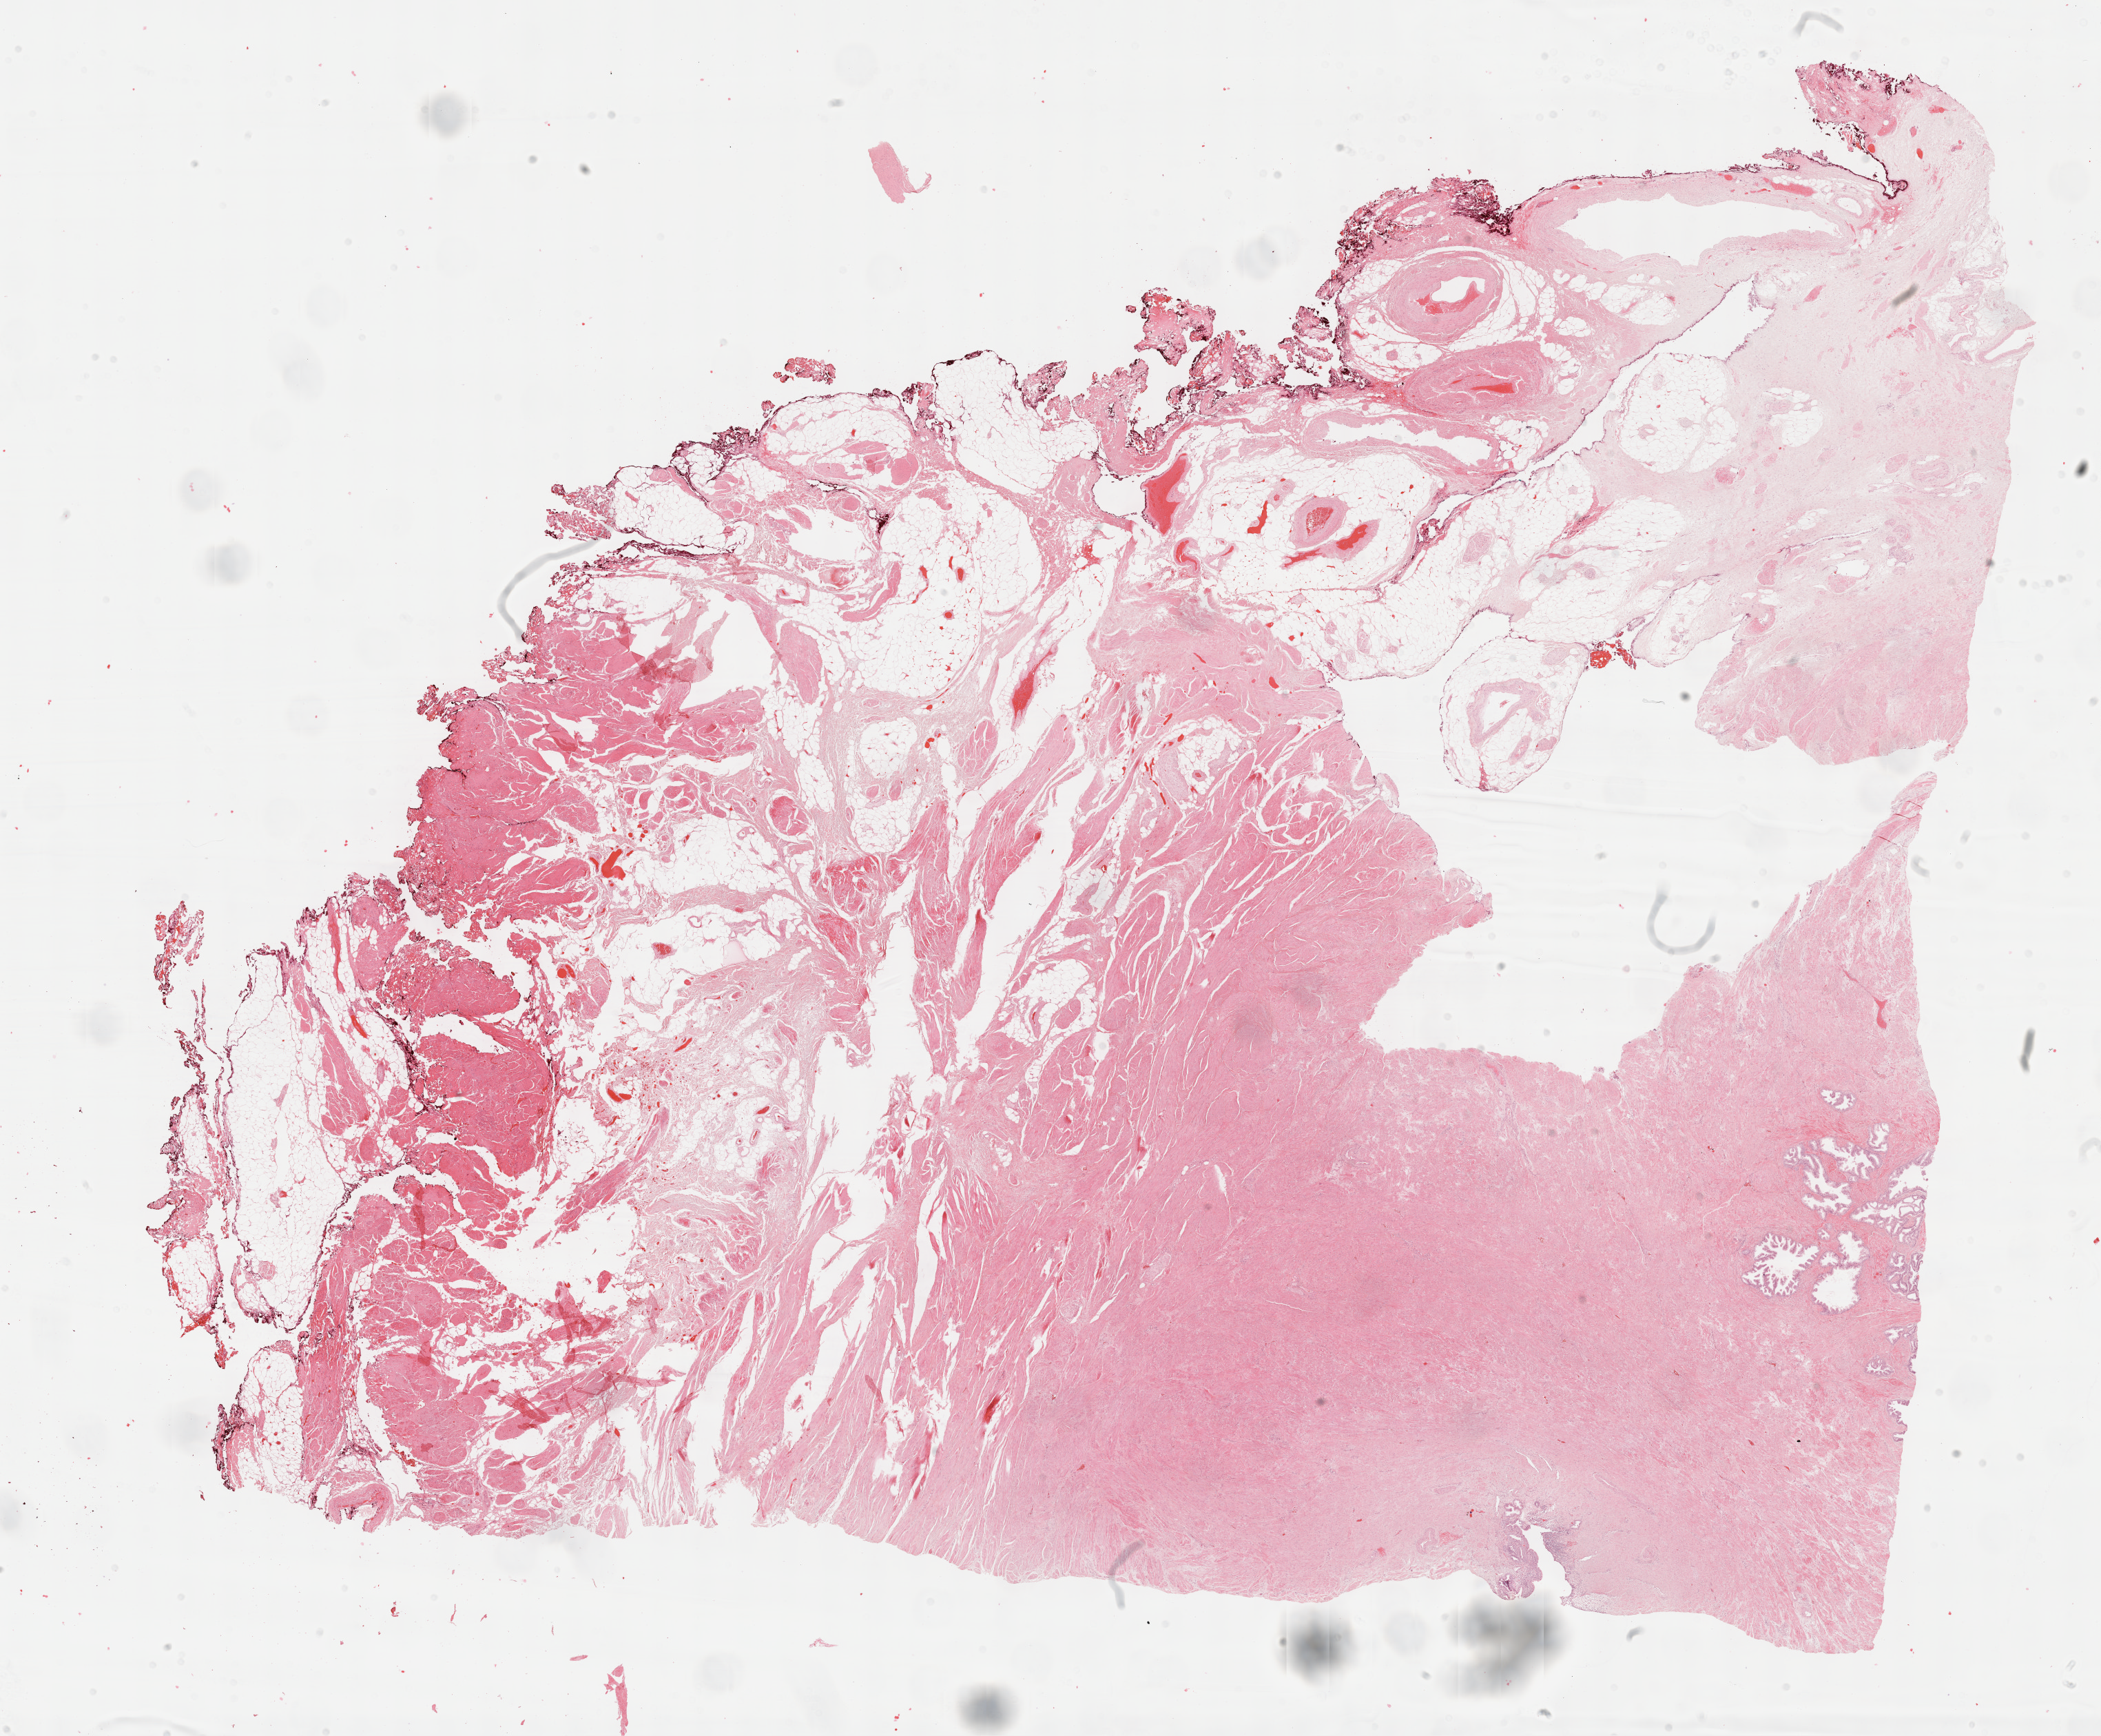
H&E whole-slide image — whole scanned area (about 24.7 x 20.4 mm) shown as a low-resolution overview, formalin-fixed paraffin-embedded (FFPE) diagnostic section, primary tumour sample from the prostate. Male, age 65 years at initial diagnosis. Gleason score: 6 (3+3).
• pathologic diagnosis: Adenocarcinoma, NOS (prostate gland)
• lymph nodes positive (case pathology): 0 of 5 examined